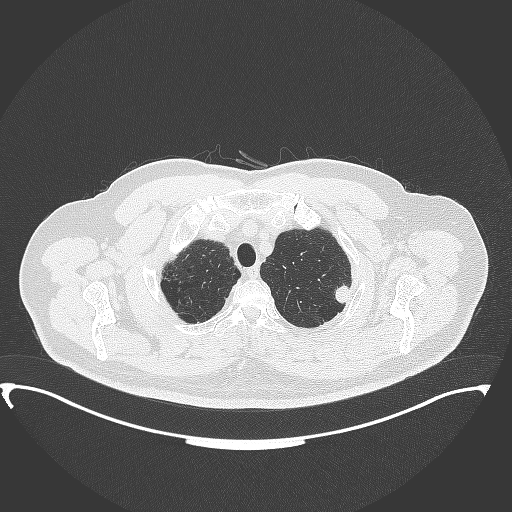
Chest CT, one axial slice. Position 323 of 350 along the scan axis. Reconstruction kernel B70f. 120 kVp. Lung window (W 1500 / L -600 HU). 1 mm slice thickness. 512 × 512 image matrix, field of view 459 × 459 mm. Male patient, age 64 years. Case-level facts recorded for this patient, not image findings: clinical TNM (as recorded): T1c N1 M1.
Structures marked on this image (rectangle marked by the reading radiologist):
- lung tumour (recorded histology: adenocarcinoma): bounding box (x1, y1, x2, y2) in pixels: (331, 282, 354, 303)